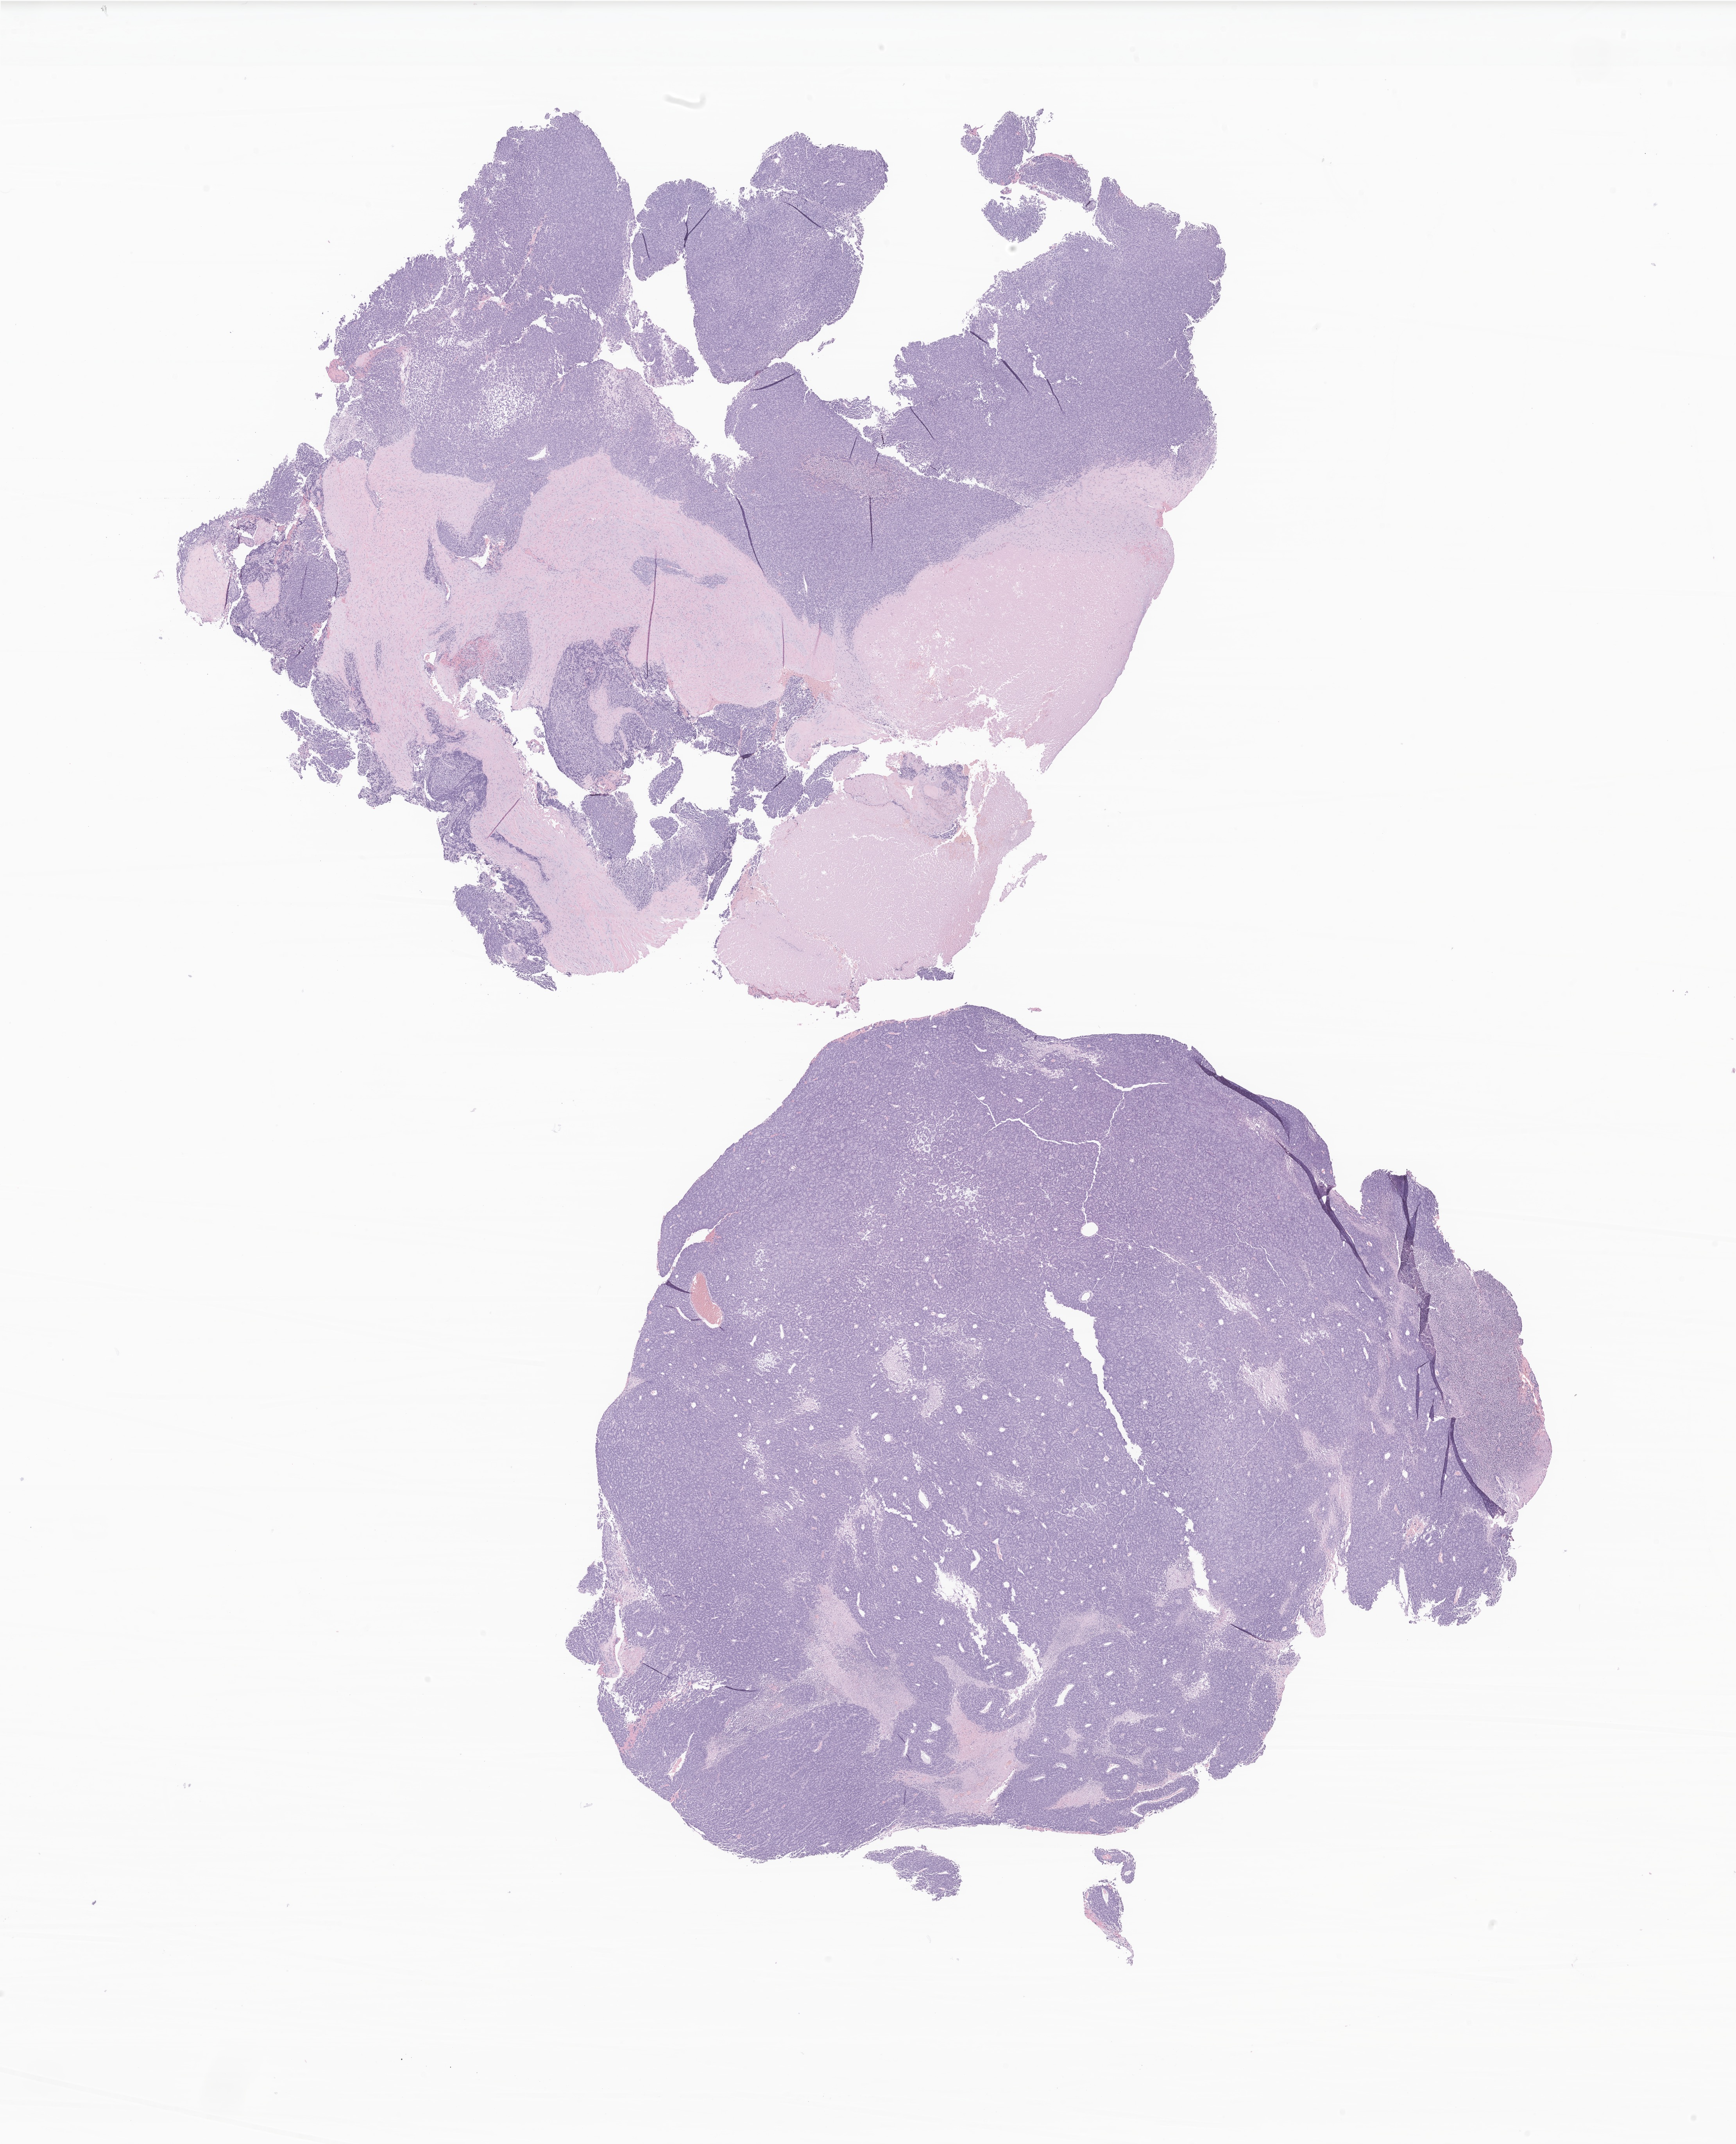
Digitized H&E-stained section of tumor tissue from the soft tissue, shown as a low-resolution overview of the whole scanned area (about 18.7 x 23.1 mm). Formalin-fixed, paraffin-embedded (FFPE) tissue. Patient: female, age 210 days.
* diagnosis (ICD-O-3 morphology term): Sarcoma, NOS